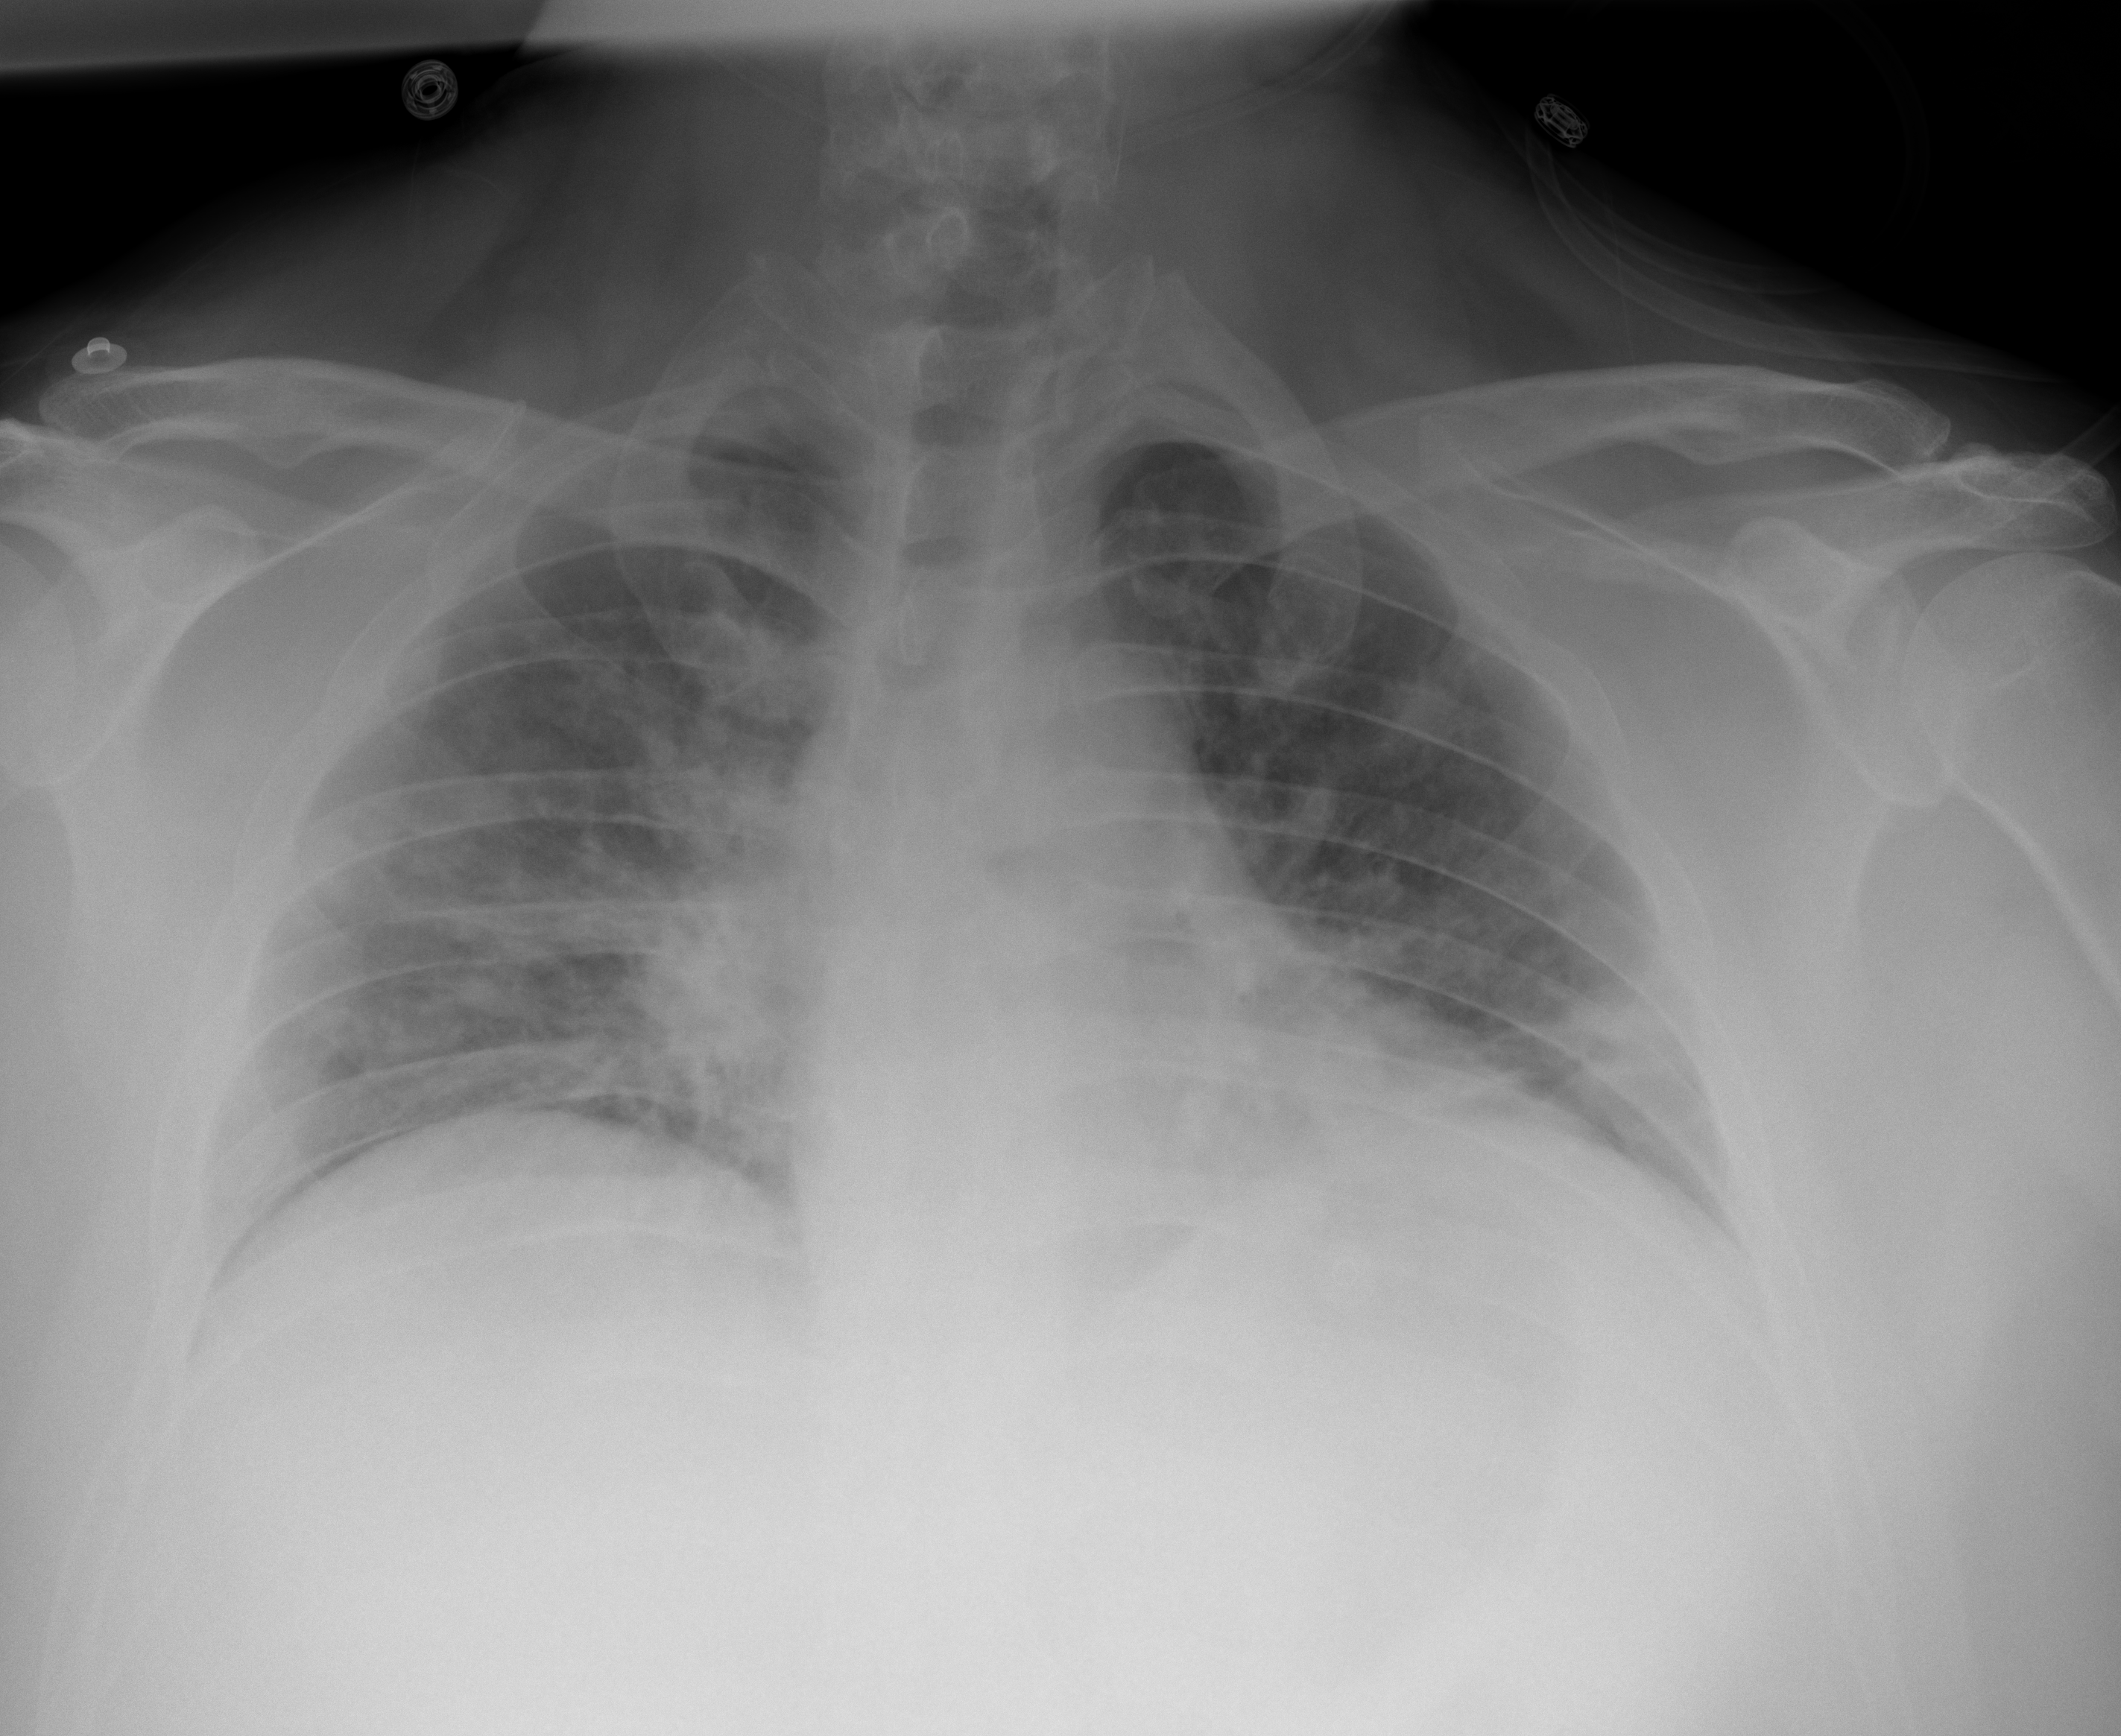
Portable chest radiograph, AP projection. Male patient, age 40 years; COVID-19 (test-positive).
Radiologist key findings (as recorded): multifocal lower lobe predominant consolidation bilaterally.